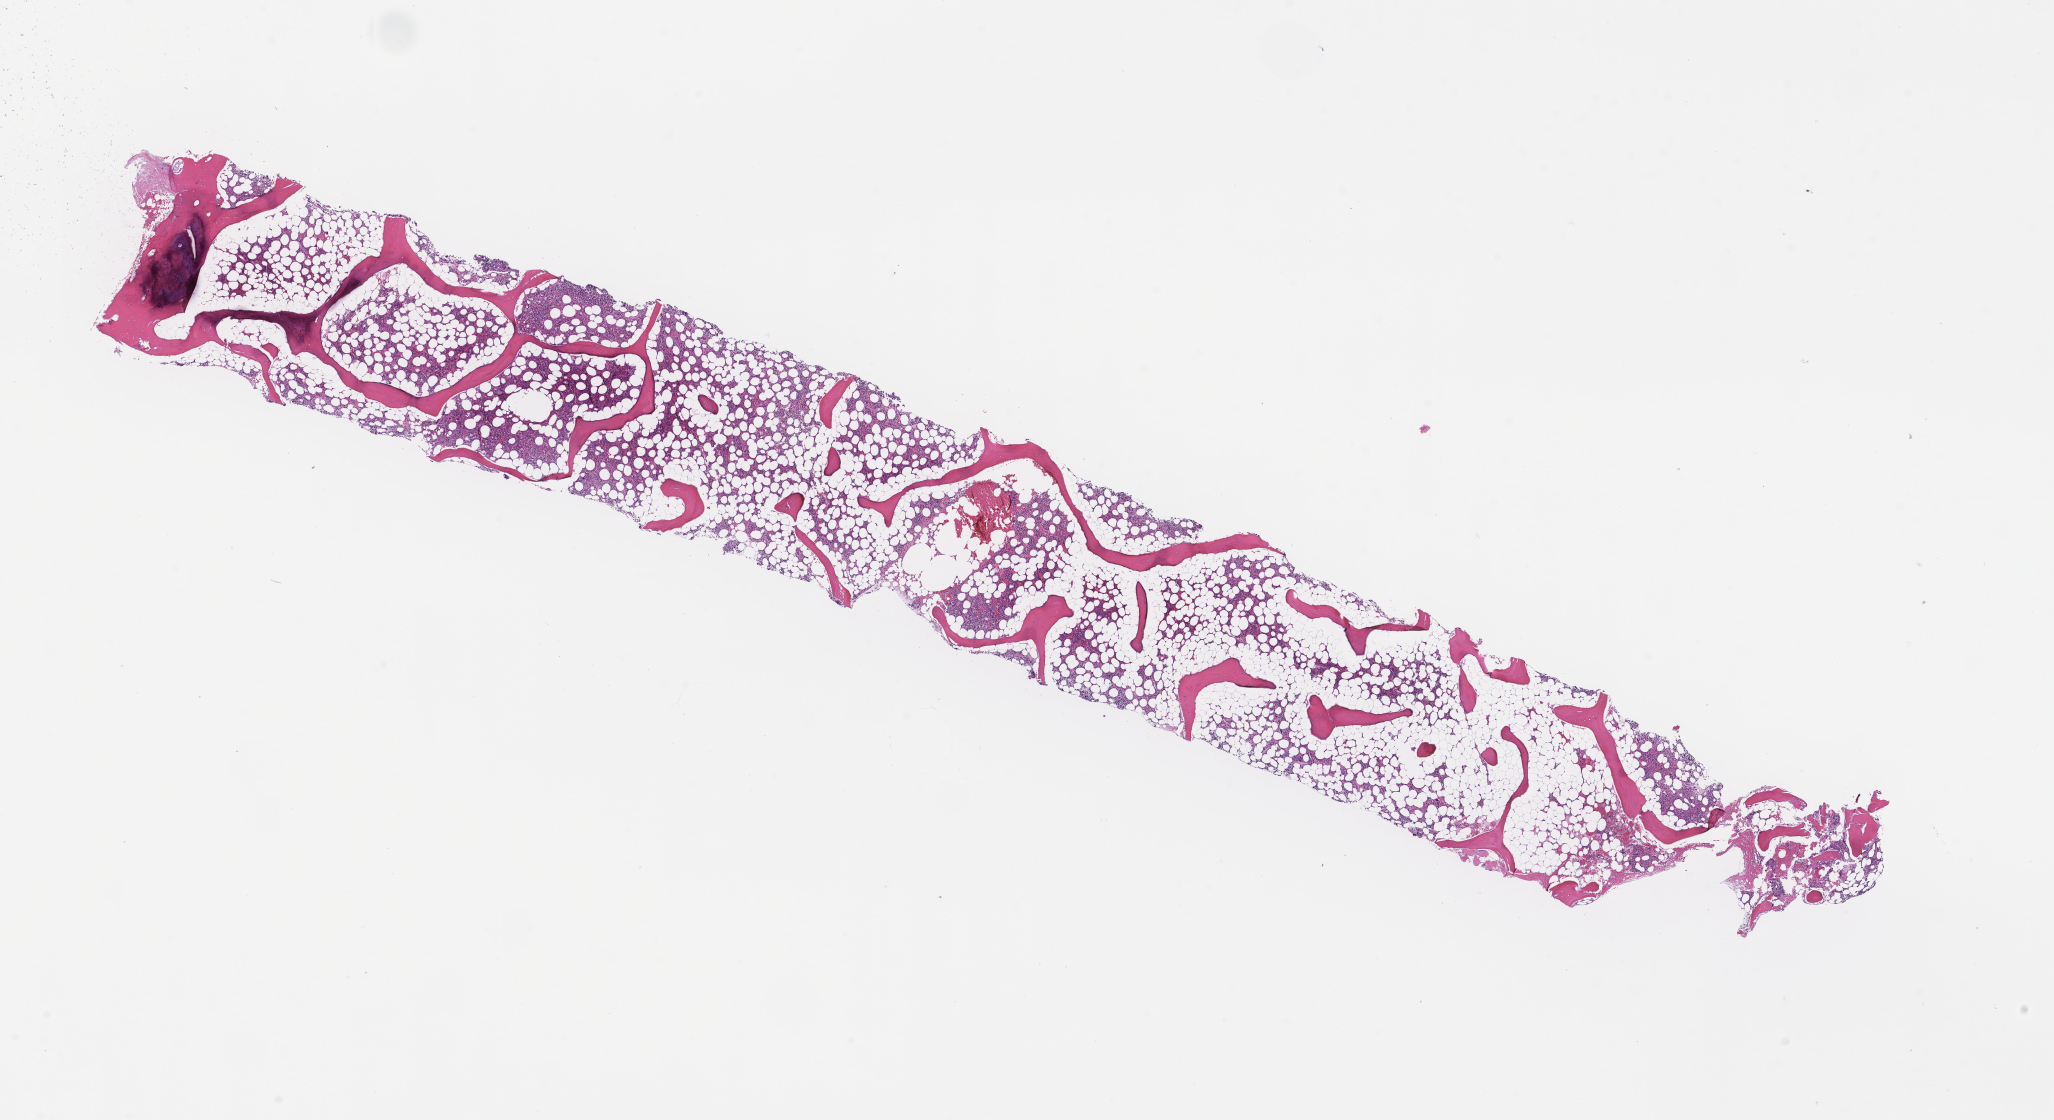
Haematoxylin and eosin whole-slide image, low-resolution overview of the scanned area, about 16.6 x 9.0 mm. FFPE section. Site: bone marrow. Patient sex: male.
This section: primary tumor. Diagnosis: Plasma Cell Myeloma.